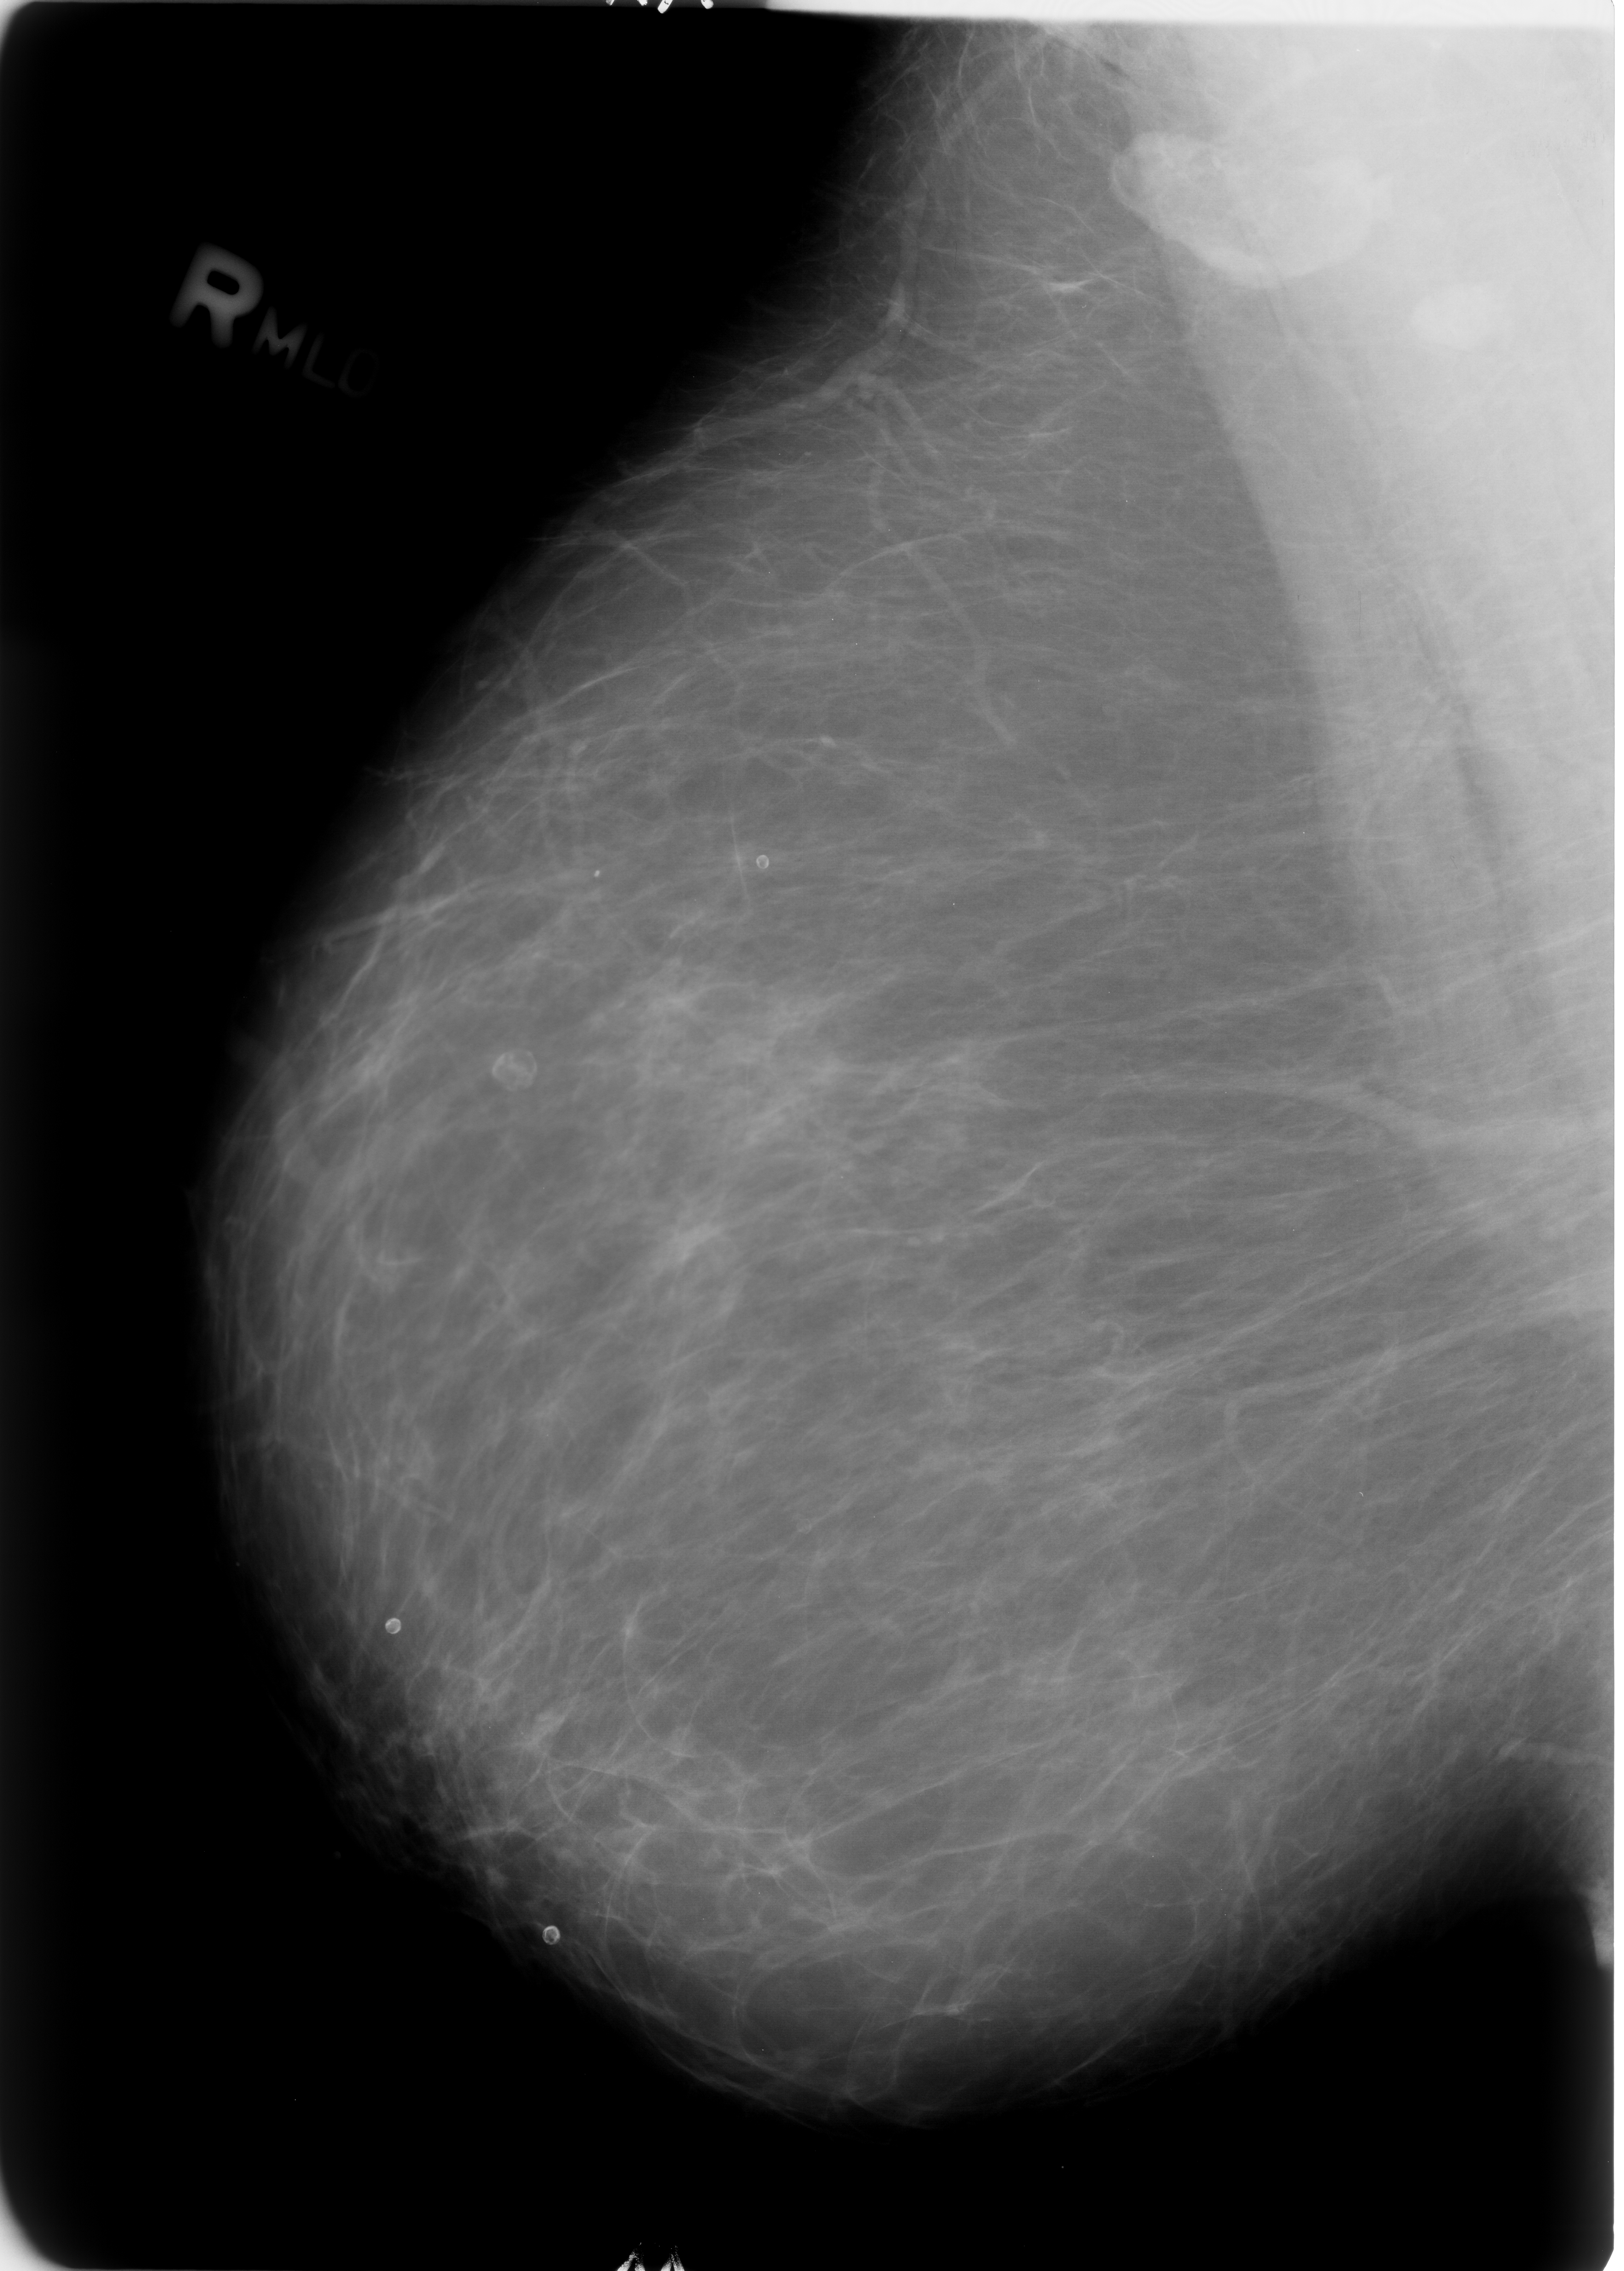
Mammogram (digitized film); right breast; mediolateral oblique (MLO) view; BI-RADS breast density category 1 (scale 1–4).
- Marked findings (only marked abnormalities are described; nothing is implied about the rest of the image): Finding 1 of 2: calcifications, morphology eggshell; BI-RADS assessment category 2; benign without callback (not worked up further).
- Finding 2 of 2: calcifications, morphology eggshell; BI-RADS assessment category 2; benign; no additional work-up was recommended (benign without callback).